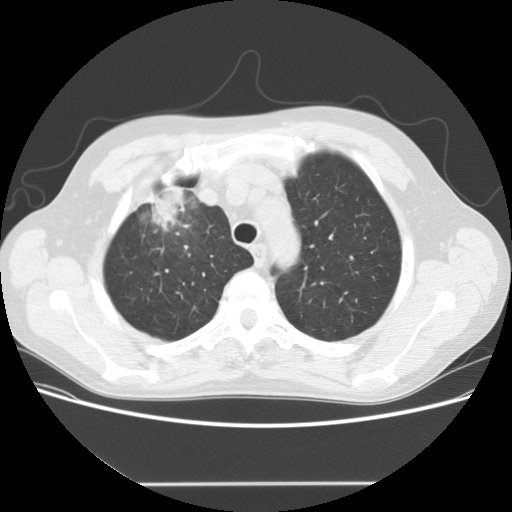
Axial slice from a low-dose chest CT screening exam; baseline annual screen; lung window (W 1500 / L -600 HU); 2.5 mm slice thickness; 120 kVp; 512 × 512 image matrix, field of view 360 × 360 mm. Male, age 56 years at enrolment. Current smoker at enrolment.
Expert reader's lesion annotation, bounding box [x1, y1, x2, y2] px = [128, 176, 208, 241]. The screening reader recorded 2 non-calcified nodules or masses ≥4 mm on this exam; which of them this box marks is not recorded.